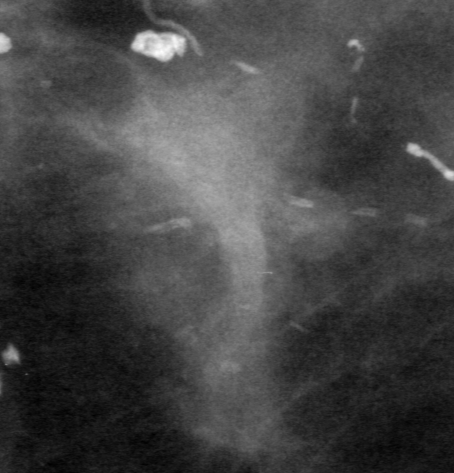
Cropped region of a digitized screen-film mammogram centred on a radiologist-marked abnormality, left breast, CC view.
Marked abnormality: mass, shape irregular, margins ill defined; BI-RADS assessment category 3; subtlety rating 3 on a 1 (subtle) to 5 (obvious) scale; pathology result (as recorded, not read from the image): malignant.